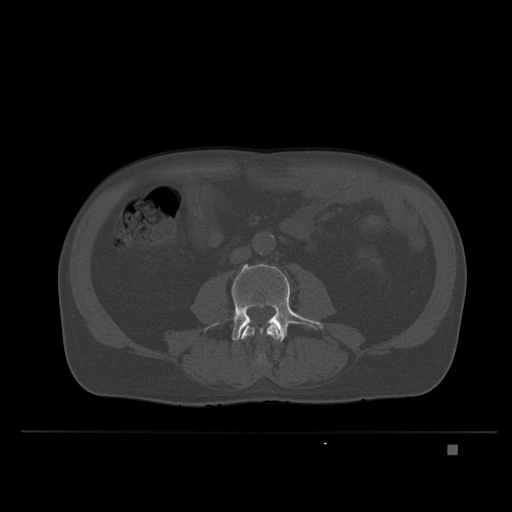
CT including the spine, one axial slice; position 82 of 435 along the scan axis; bone window (W 1800 / L 400 HU); 512 × 512 image matrix, field of view 434 × 434 mm. Patient: male, 73 years. From the clinical record (not read from this slice): primary cancer: skin.
Structures marked on this image (semi-automatically segmented with operator editing):
- L3 vertebra: bounding box (x1, y1, x2, y2) in pixels: (241, 321, 282, 365)
- L4 vertebra: (209, 264, 323, 353)